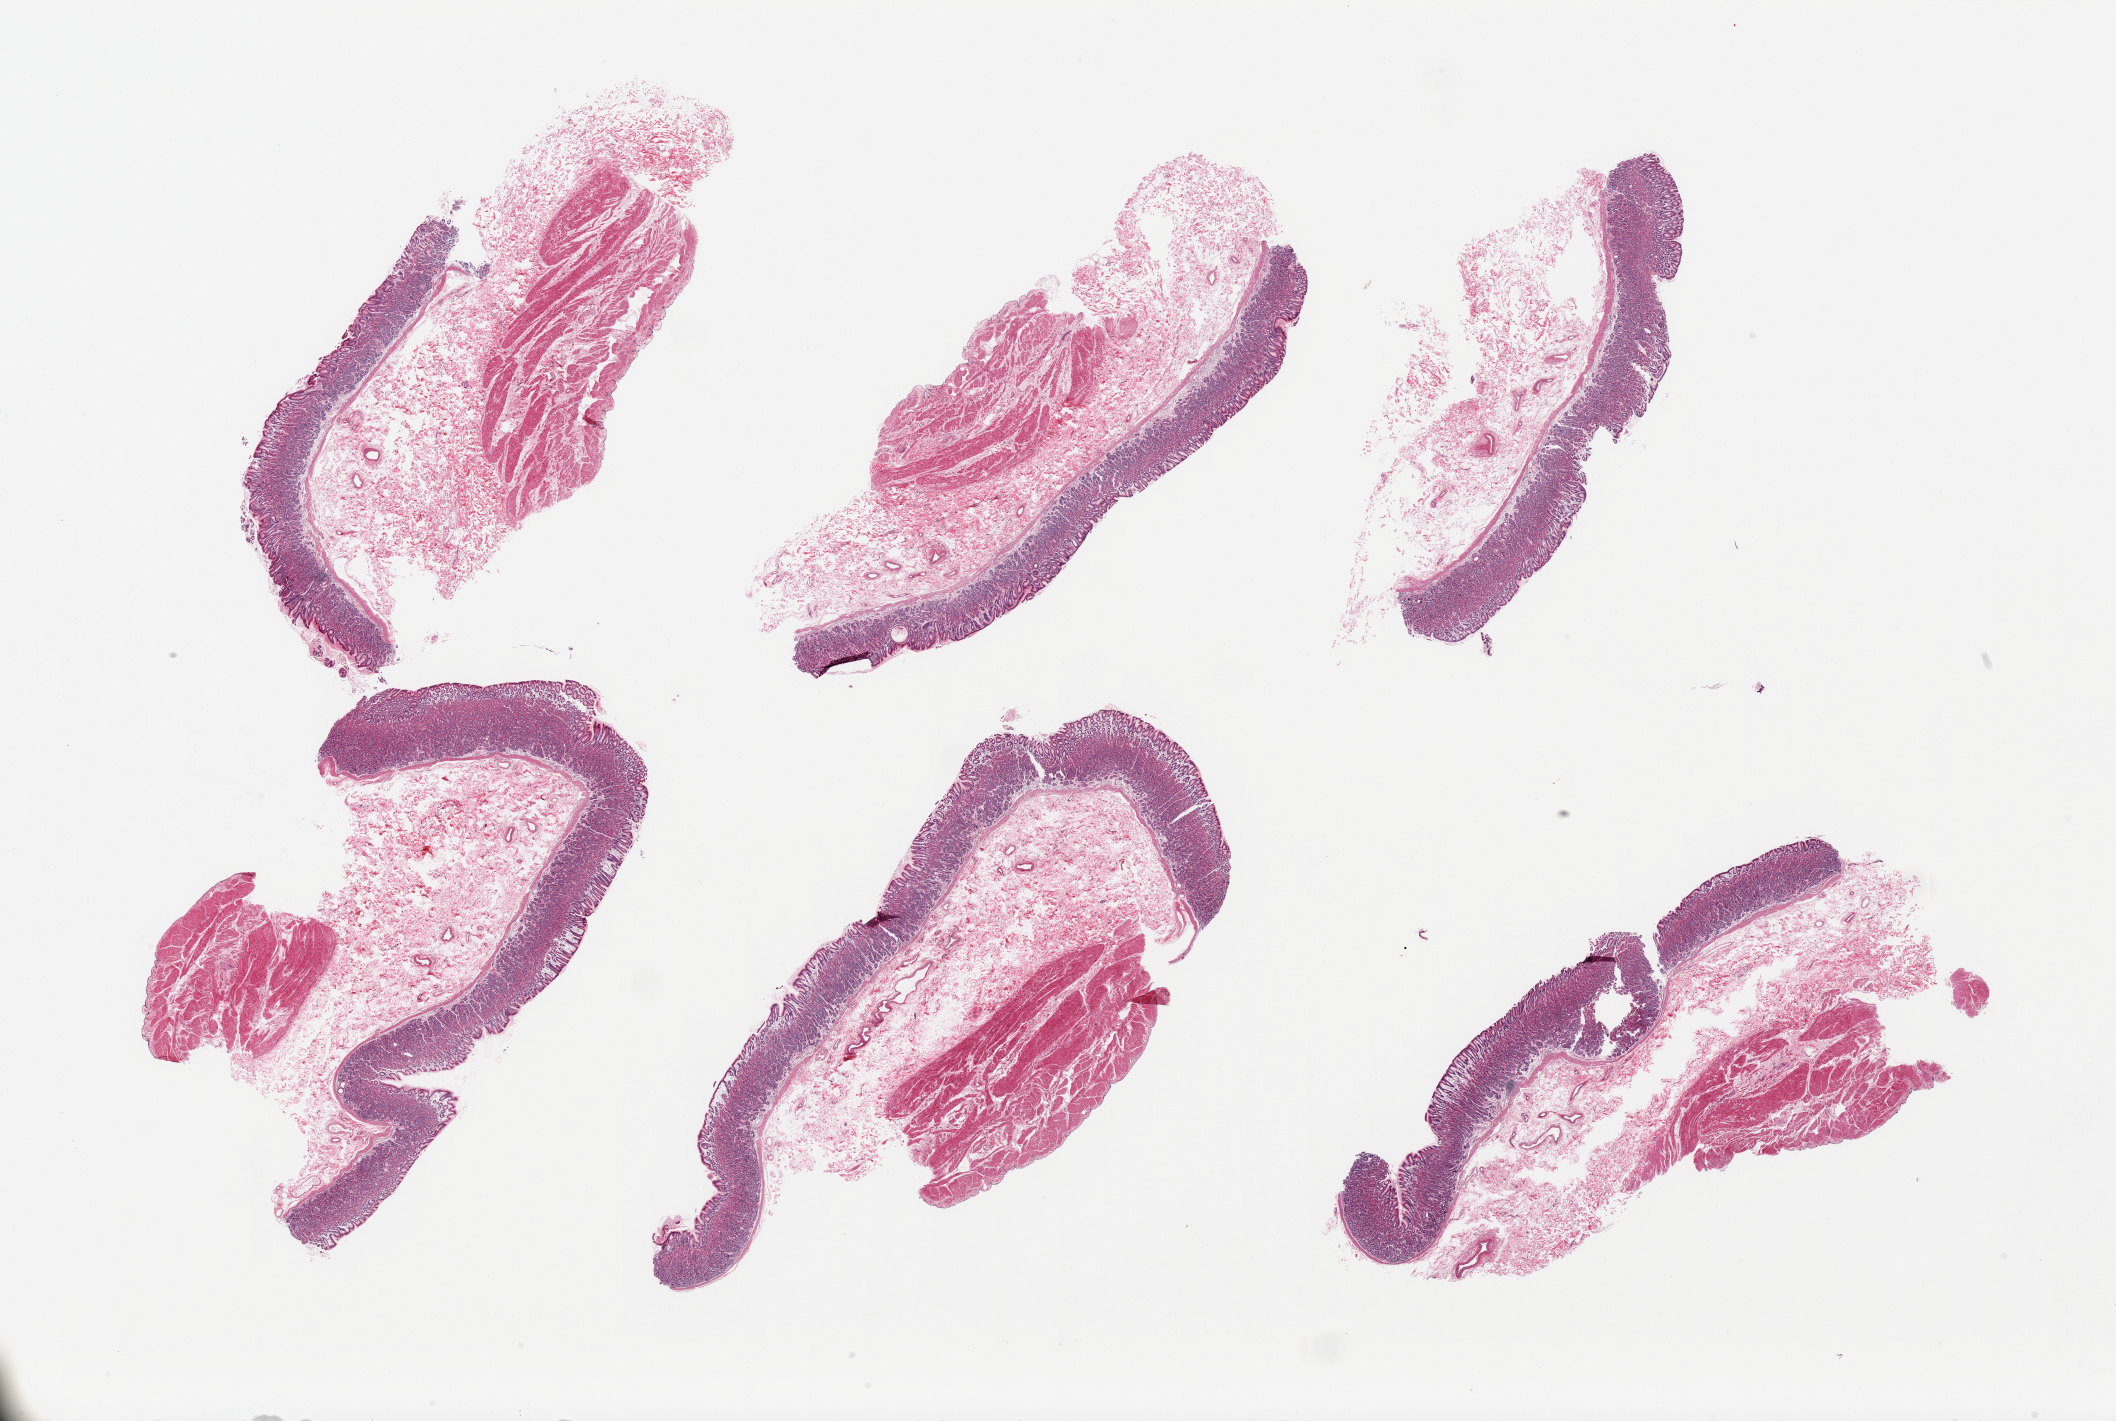
Digitized haematoxylin and eosin-stained section — shown as a low-resolution overview of the whole scanned area (about 33.5 x 22.5 mm); PAXgene-fixed paraffin-embedded (PFPE) section; section of stomach (target tissue); tissue donor sample.
Review note (as recorded): 6 pieces, 1 without muscularis; edematous submucosa & deep mucosa.